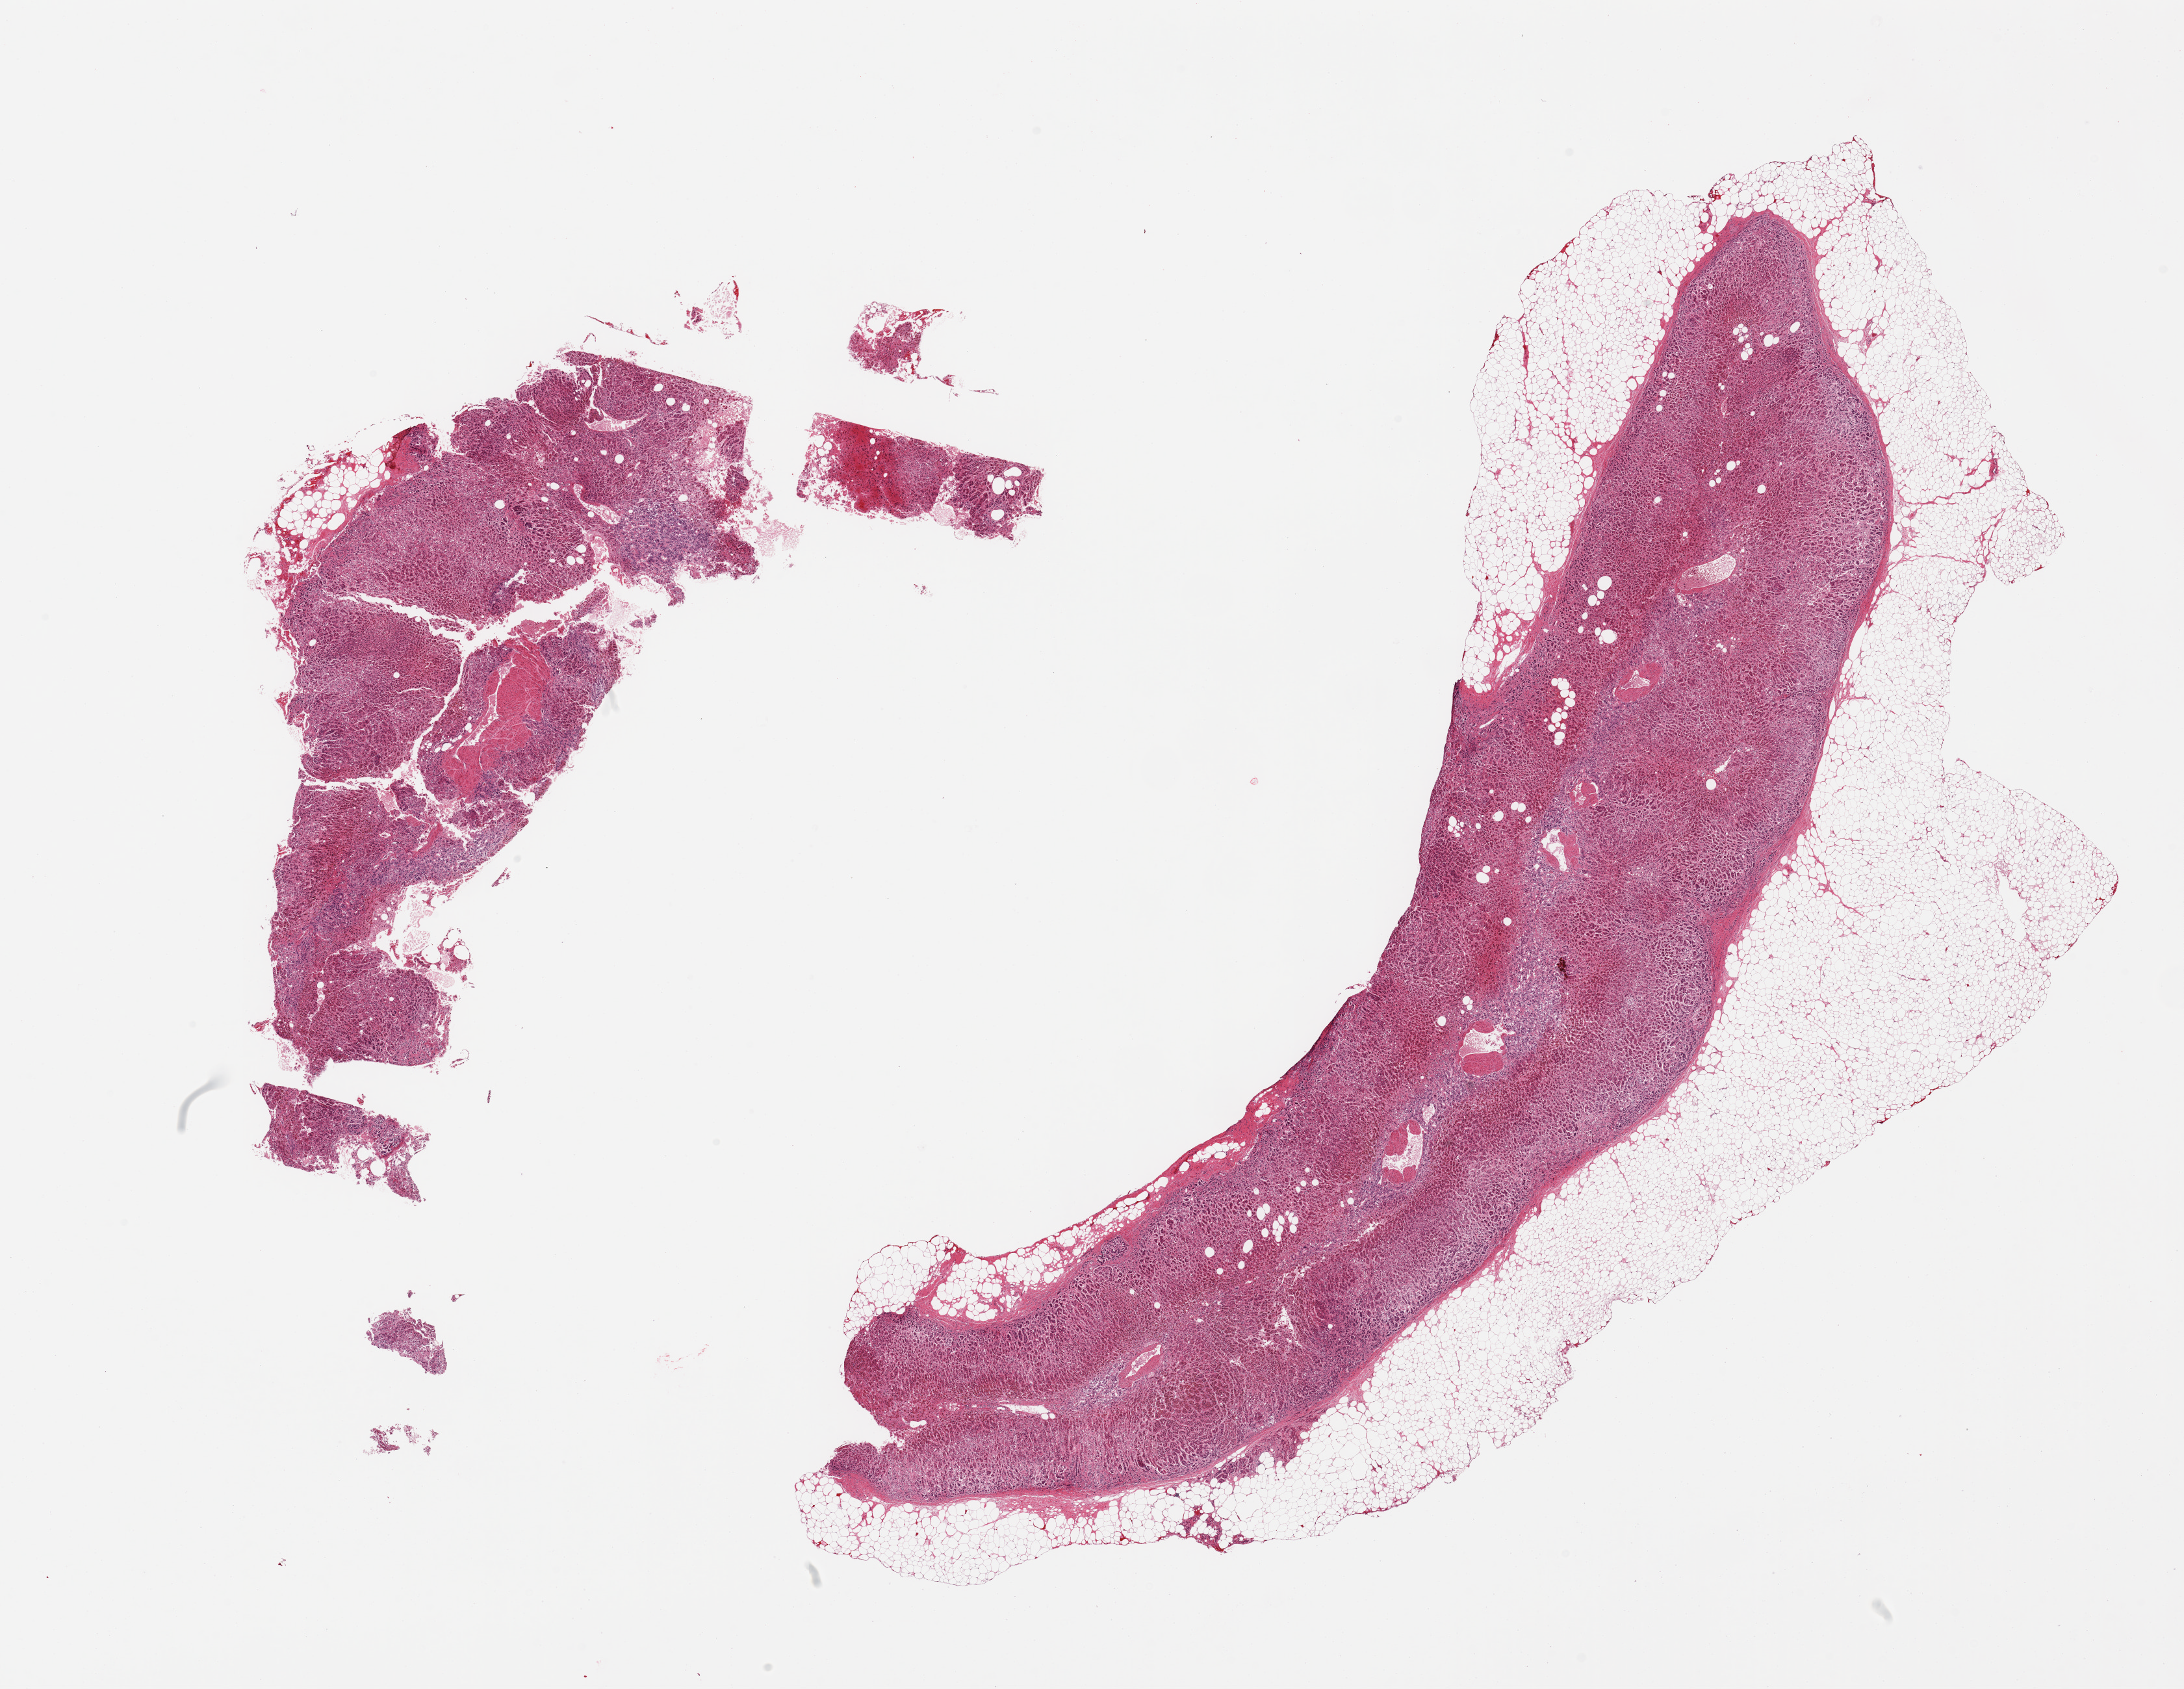
Whole-slide image, hematoxylin and eosin (H&E) stain, brightfield — a low-resolution overview of the entire scanned area, about 26.6 x 20.6 mm (acquisition: 20x scan); PAXgene-fixed paraffin-embedded (PFPE) section; target tissue: adrenal gland; donor tissue sample. Donor: male.
Reviewer comment on this tissue sample: 2 pieces; cortex and medulla; one piece includes ~40% external fat.